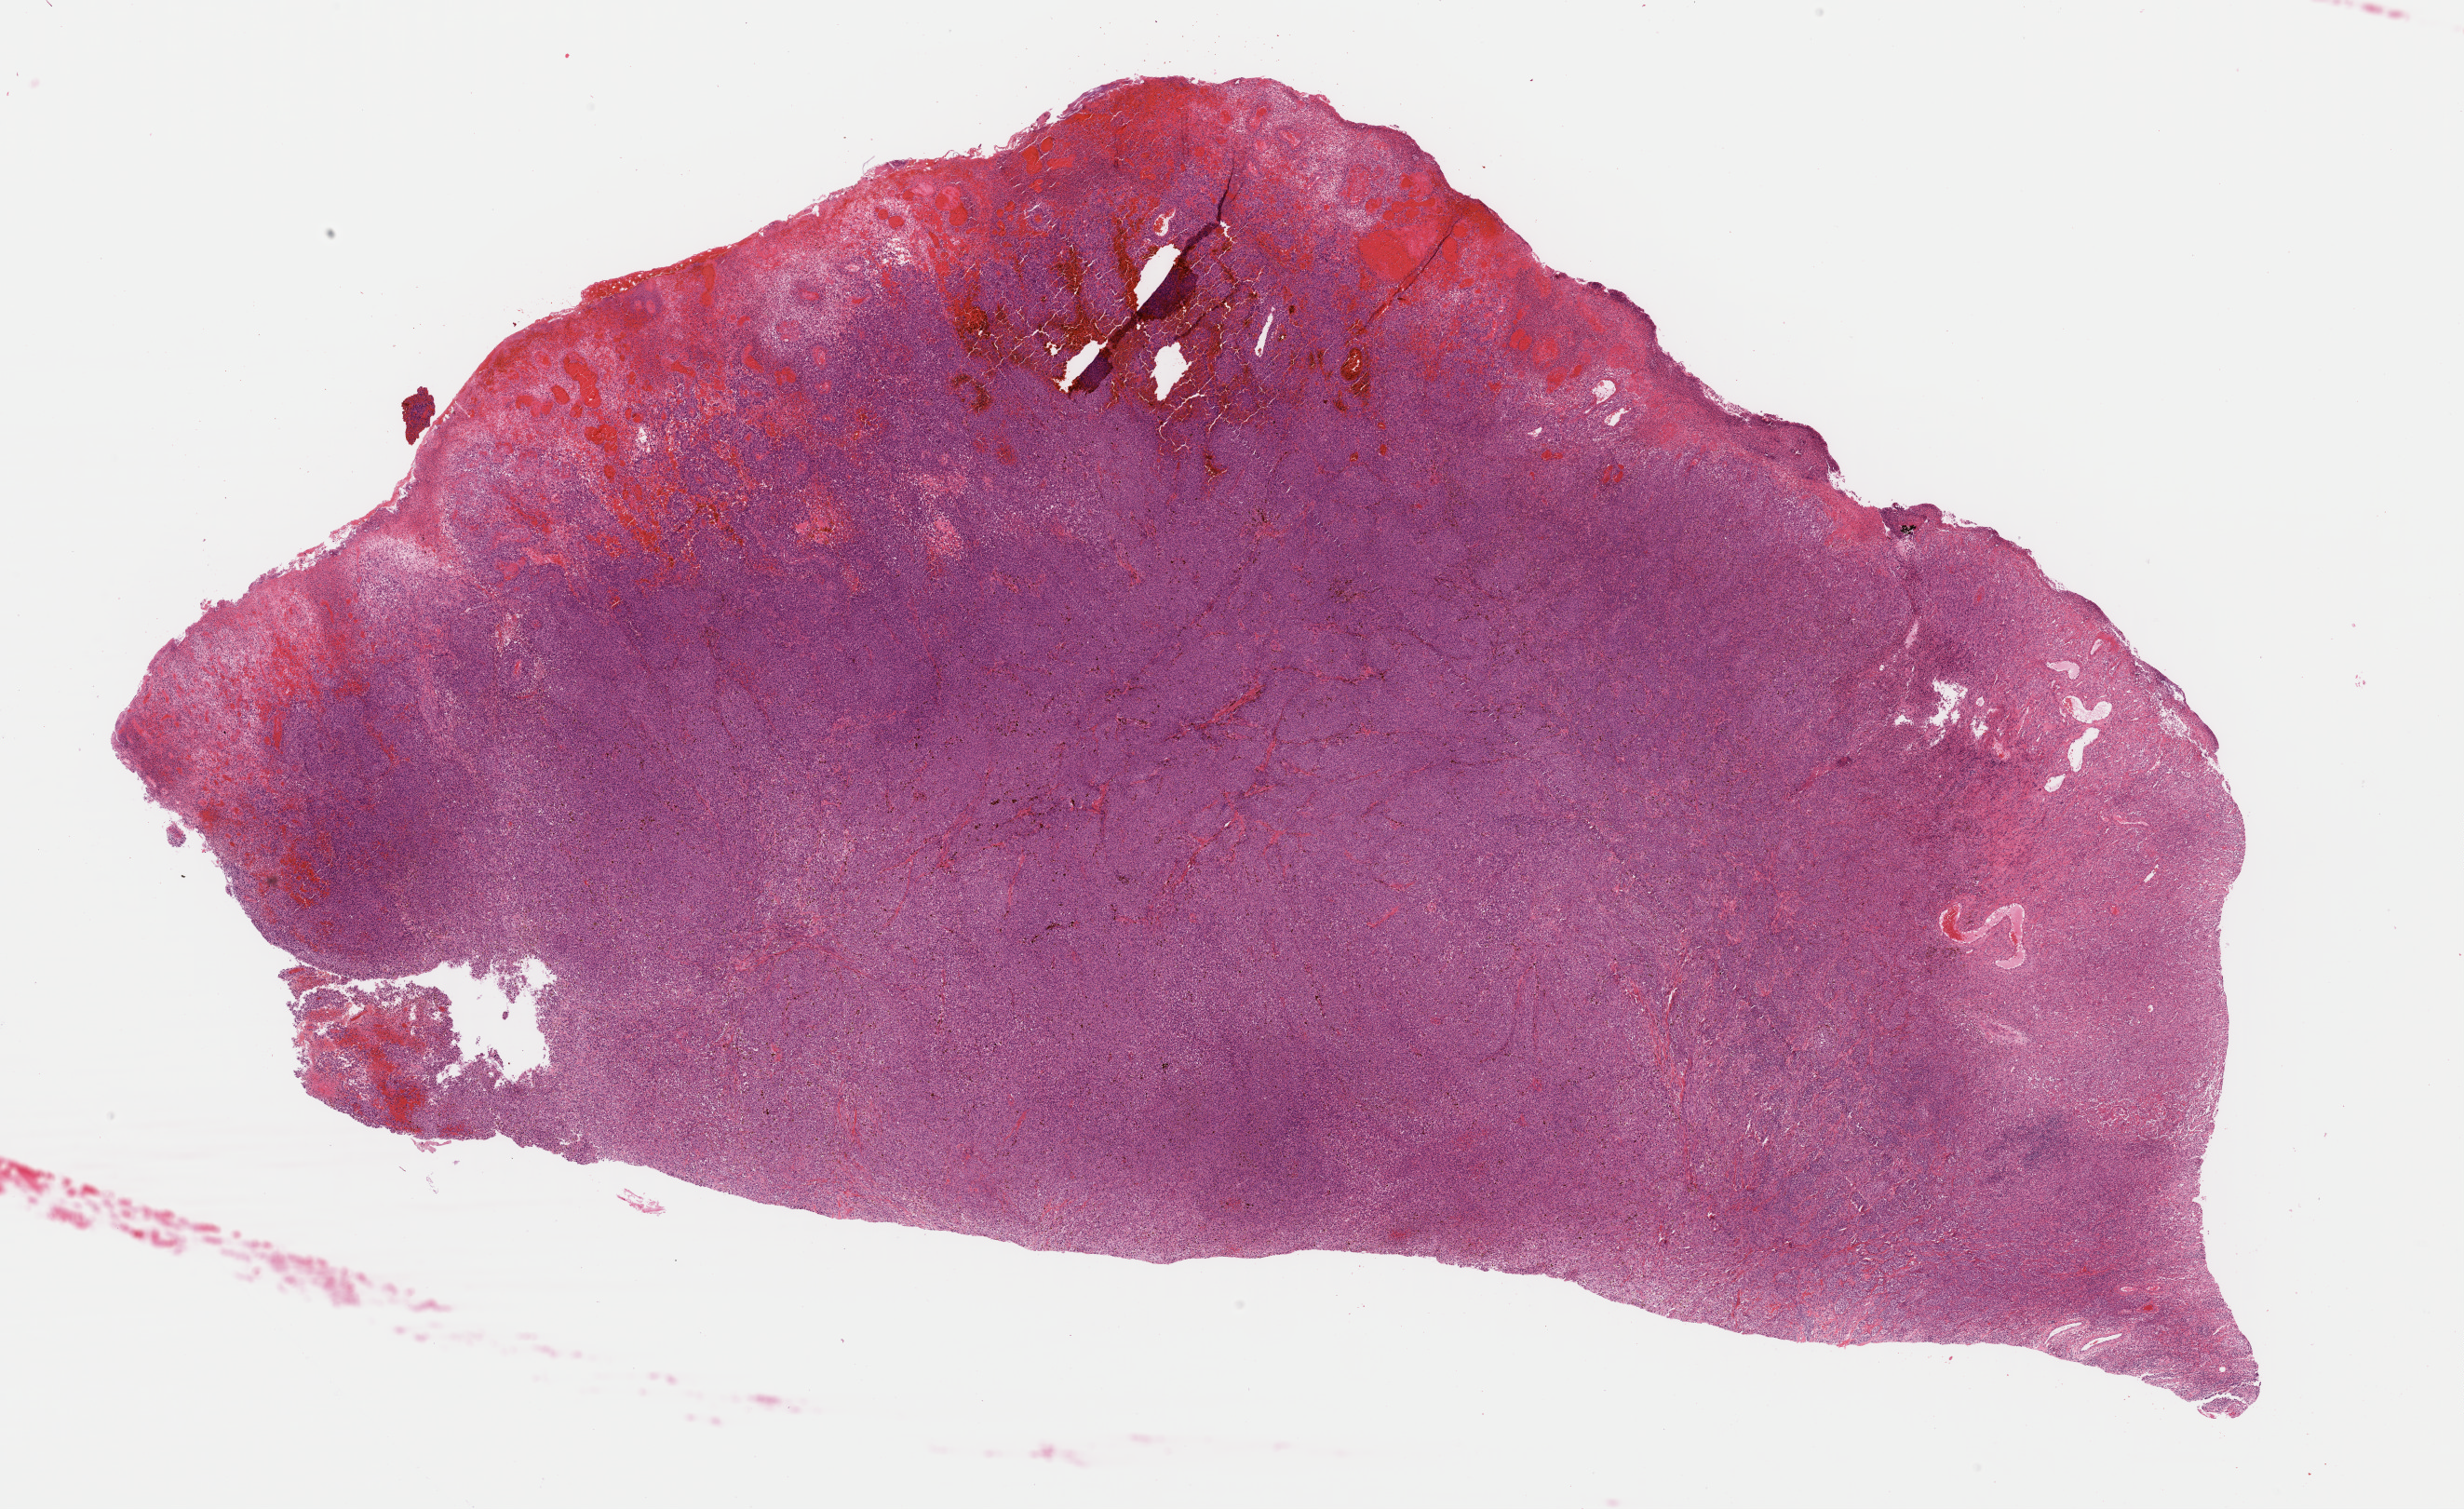
Whole-slide histology image, H&E — whole scanned area (about 20.9 x 12.8 mm, acquisition: 40x scan) shown as a low-resolution overview, formalin-fixed paraffin-embedded (FFPE) diagnostic section, sample: primary tumour, skin. Female patient; age at initial diagnosis 73 years.
AJCC pathologic stage: IIC (7th edition). Pathologic diagnosis: Malignant melanoma, NOS.